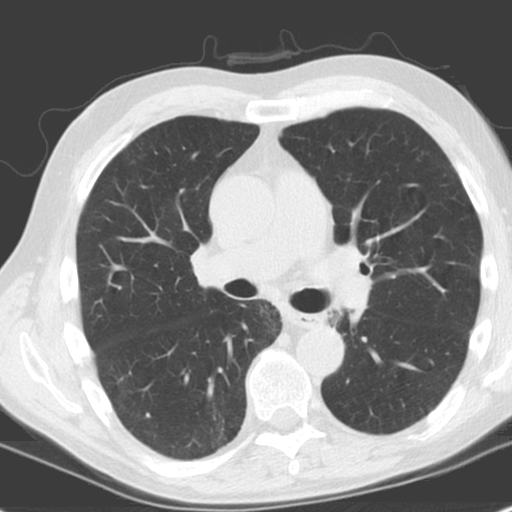
Chest CT (low-dose screening protocol), one axial image; baseline screening round; lung window (W 1500 / L -600 HU); 3.2 mm slice thickness; standard (soft-tissue) reconstruction kernel (C); slice 77 of 185 in the series; 512 × 512 image matrix, field of view 321 × 321 mm. Male, age 61 years at enrolment. Former smoker at enrolment.
Expert reader's lesion annotation, bounding box (x1, y1, x2, y2) in pixels: (310, 303, 355, 341). Screening reader's record for this exam: no non-calcified nodule ≥4 mm recorded. Official screen result: negative screen, minor abnormalities not suspicious for lung cancer. Participant outcome: lung cancer diagnosed 1146 days after this screen (after the third annual screen) — squamous cell carcinoma, NOS, left upper lobe, left lower lobe, well differentiated (G1), stage IIB (AJCC 6th edition), 100 mm at pathology.